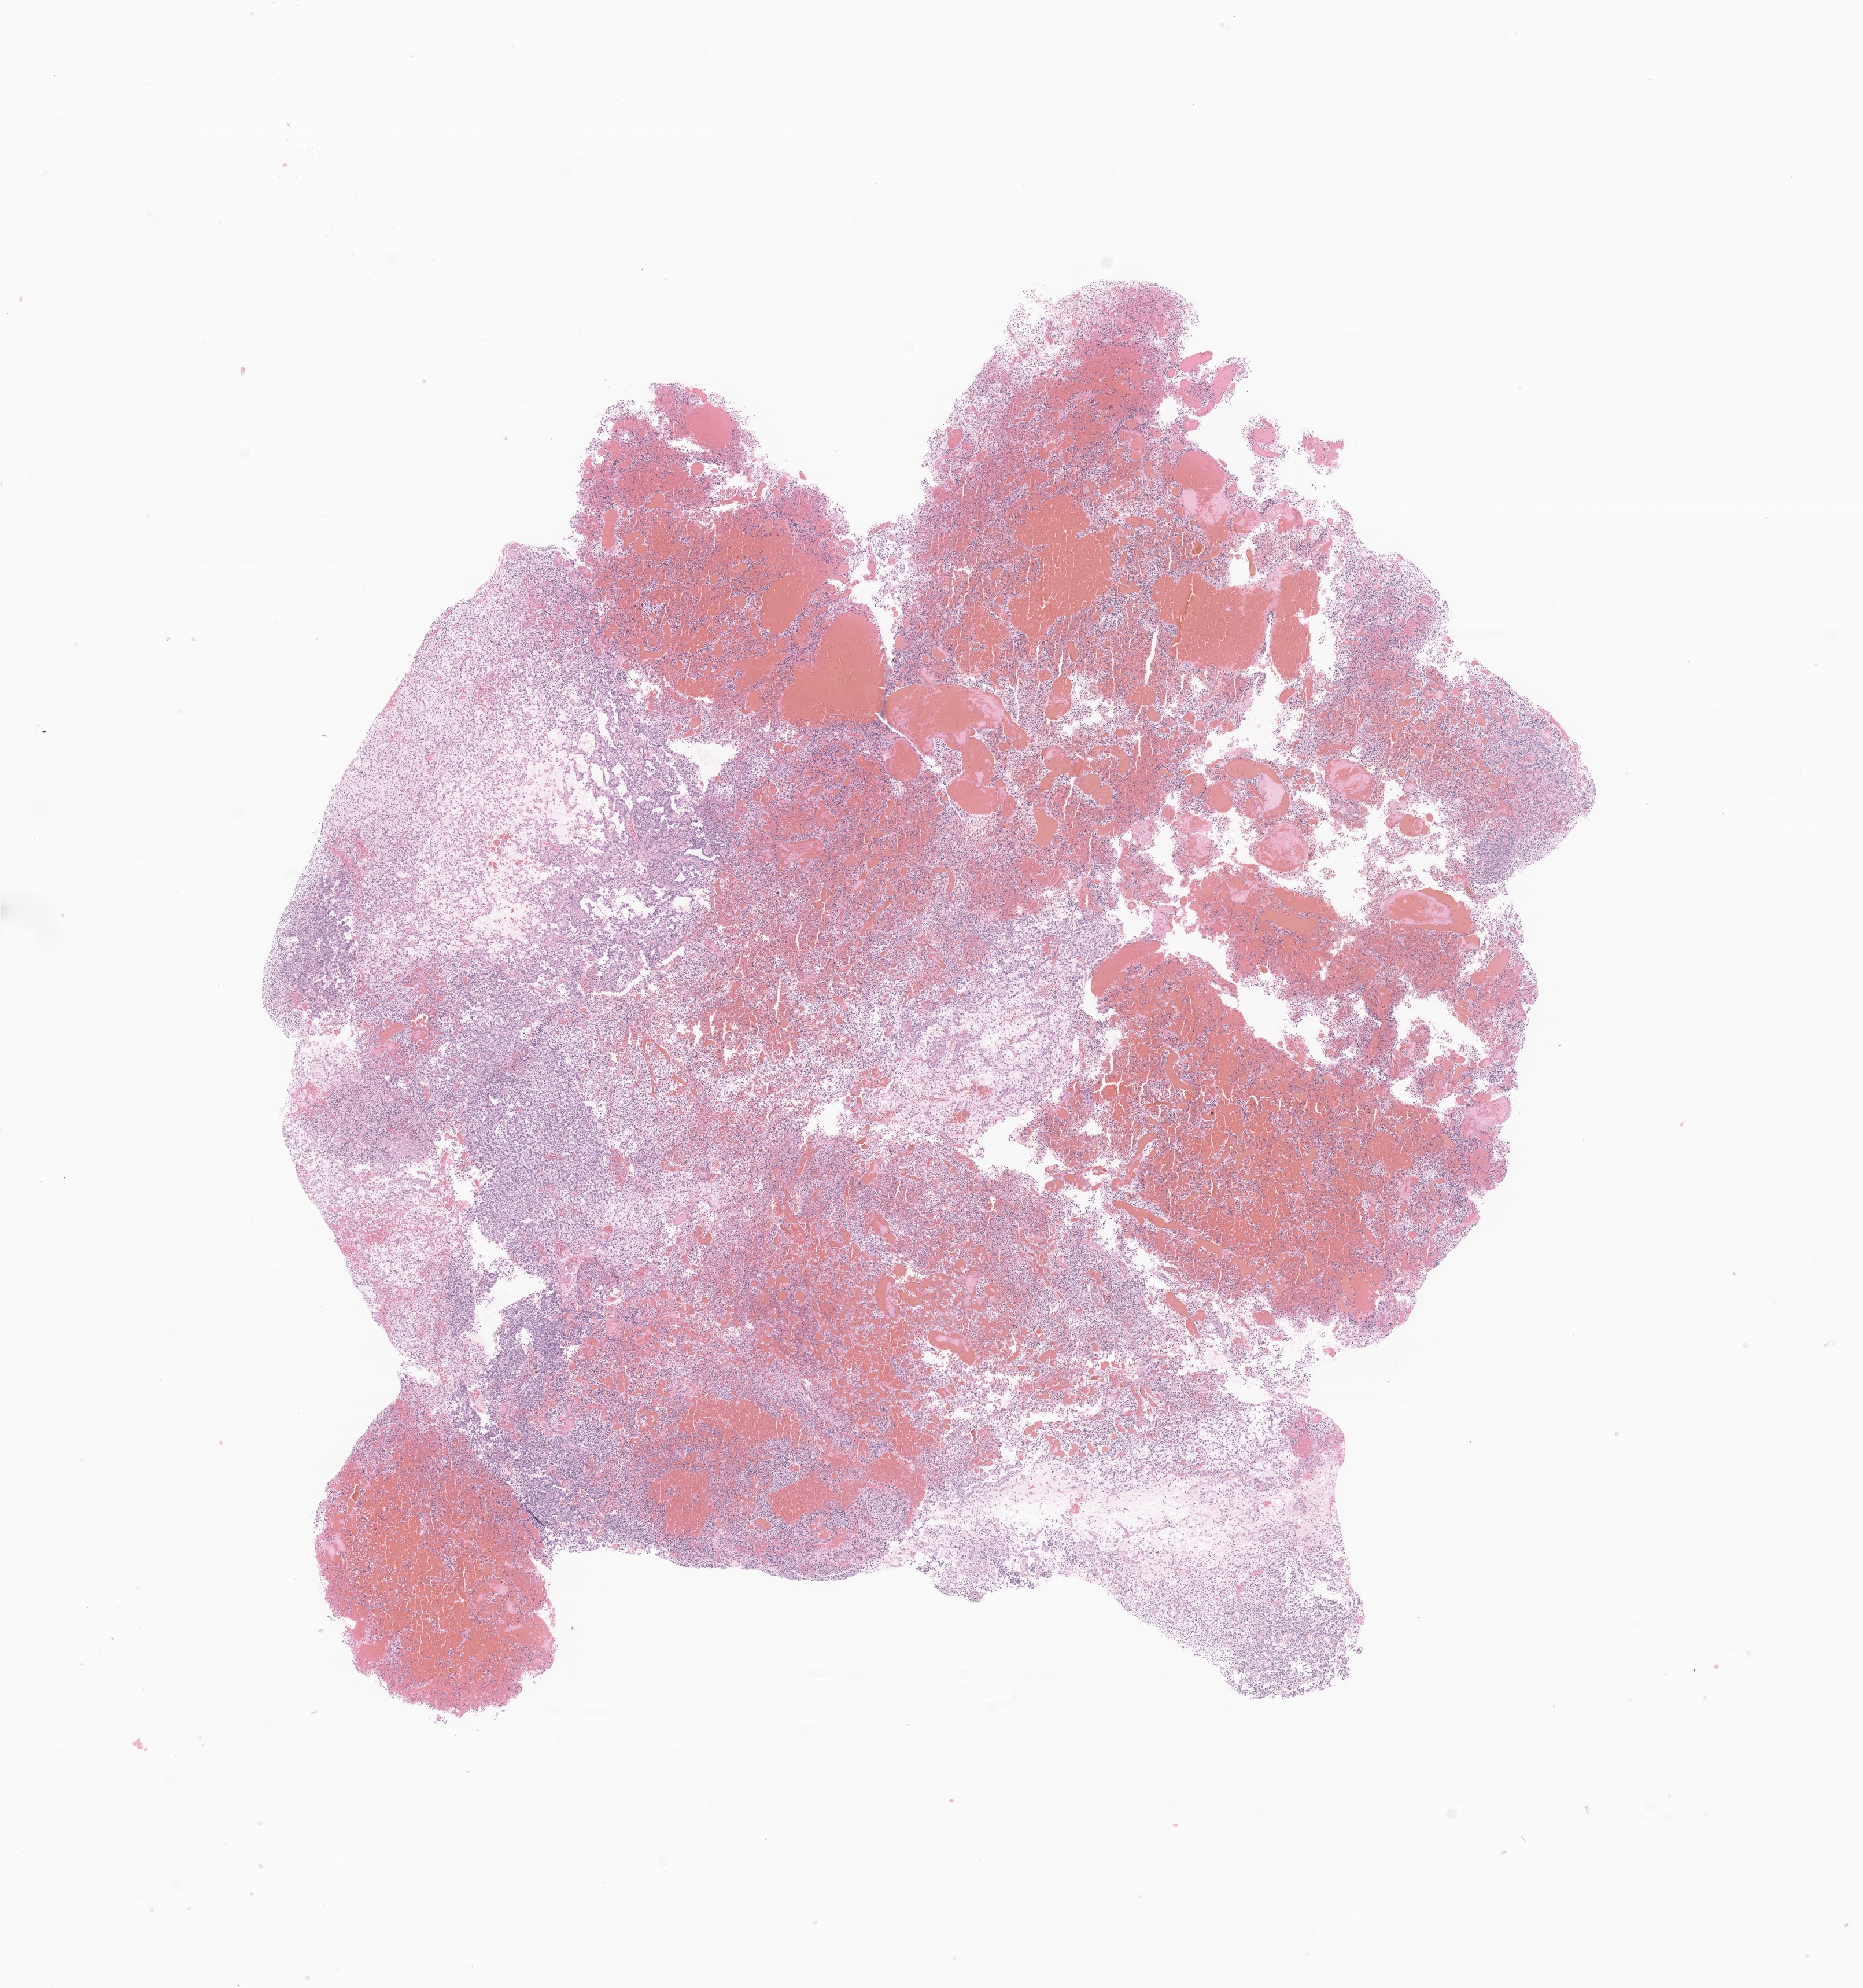
Digitized haematoxylin and eosin-stained section of tumor tissue from the brain — shown as a low-resolution overview of the whole scanned area (about 13.6 x 14.5 mm); formalin-fixed paraffin-embedded section. Male patient, age 73 months (6 years 1 month).
- diagnosis: Glioma, malignant